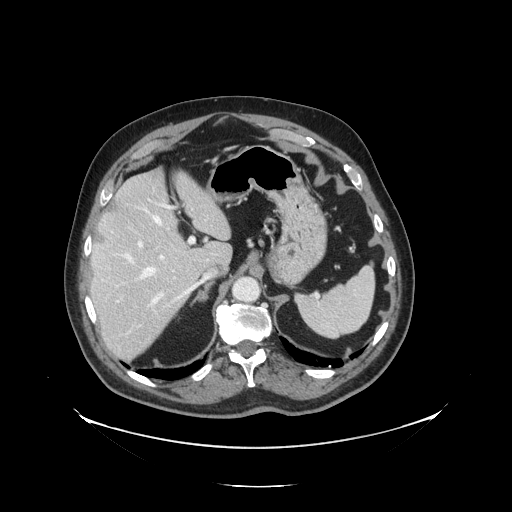
Contrast-enhanced abdominal CT, one axial slice. 120 kVp. Intravenous contrast given. Soft-tissue window (W 400 / L 40 HU). 2.5 mm slice thickness. 512 × 512 image matrix, field of view 497 × 497 mm. Male patient, age 77 years. Case-level facts recorded for this patient, not image findings: diagnosis: colorectal cancer liver metastases, imaged before liver resection; multiple liver metastases: no; largest metastasis: 1.5 cm; disease in both lobes: no.
Structures marked on this image (expert manual segmentation):
- hepatic veins: bounding box [x1, y1, x2, y2] px = [124, 209, 209, 300]
- liver: [91, 172, 231, 361]
- planned liver remnant (the part of the liver to remain after resection): [92, 172, 230, 288]
- portal vein (with intrahepatic branches): [116, 205, 194, 307]